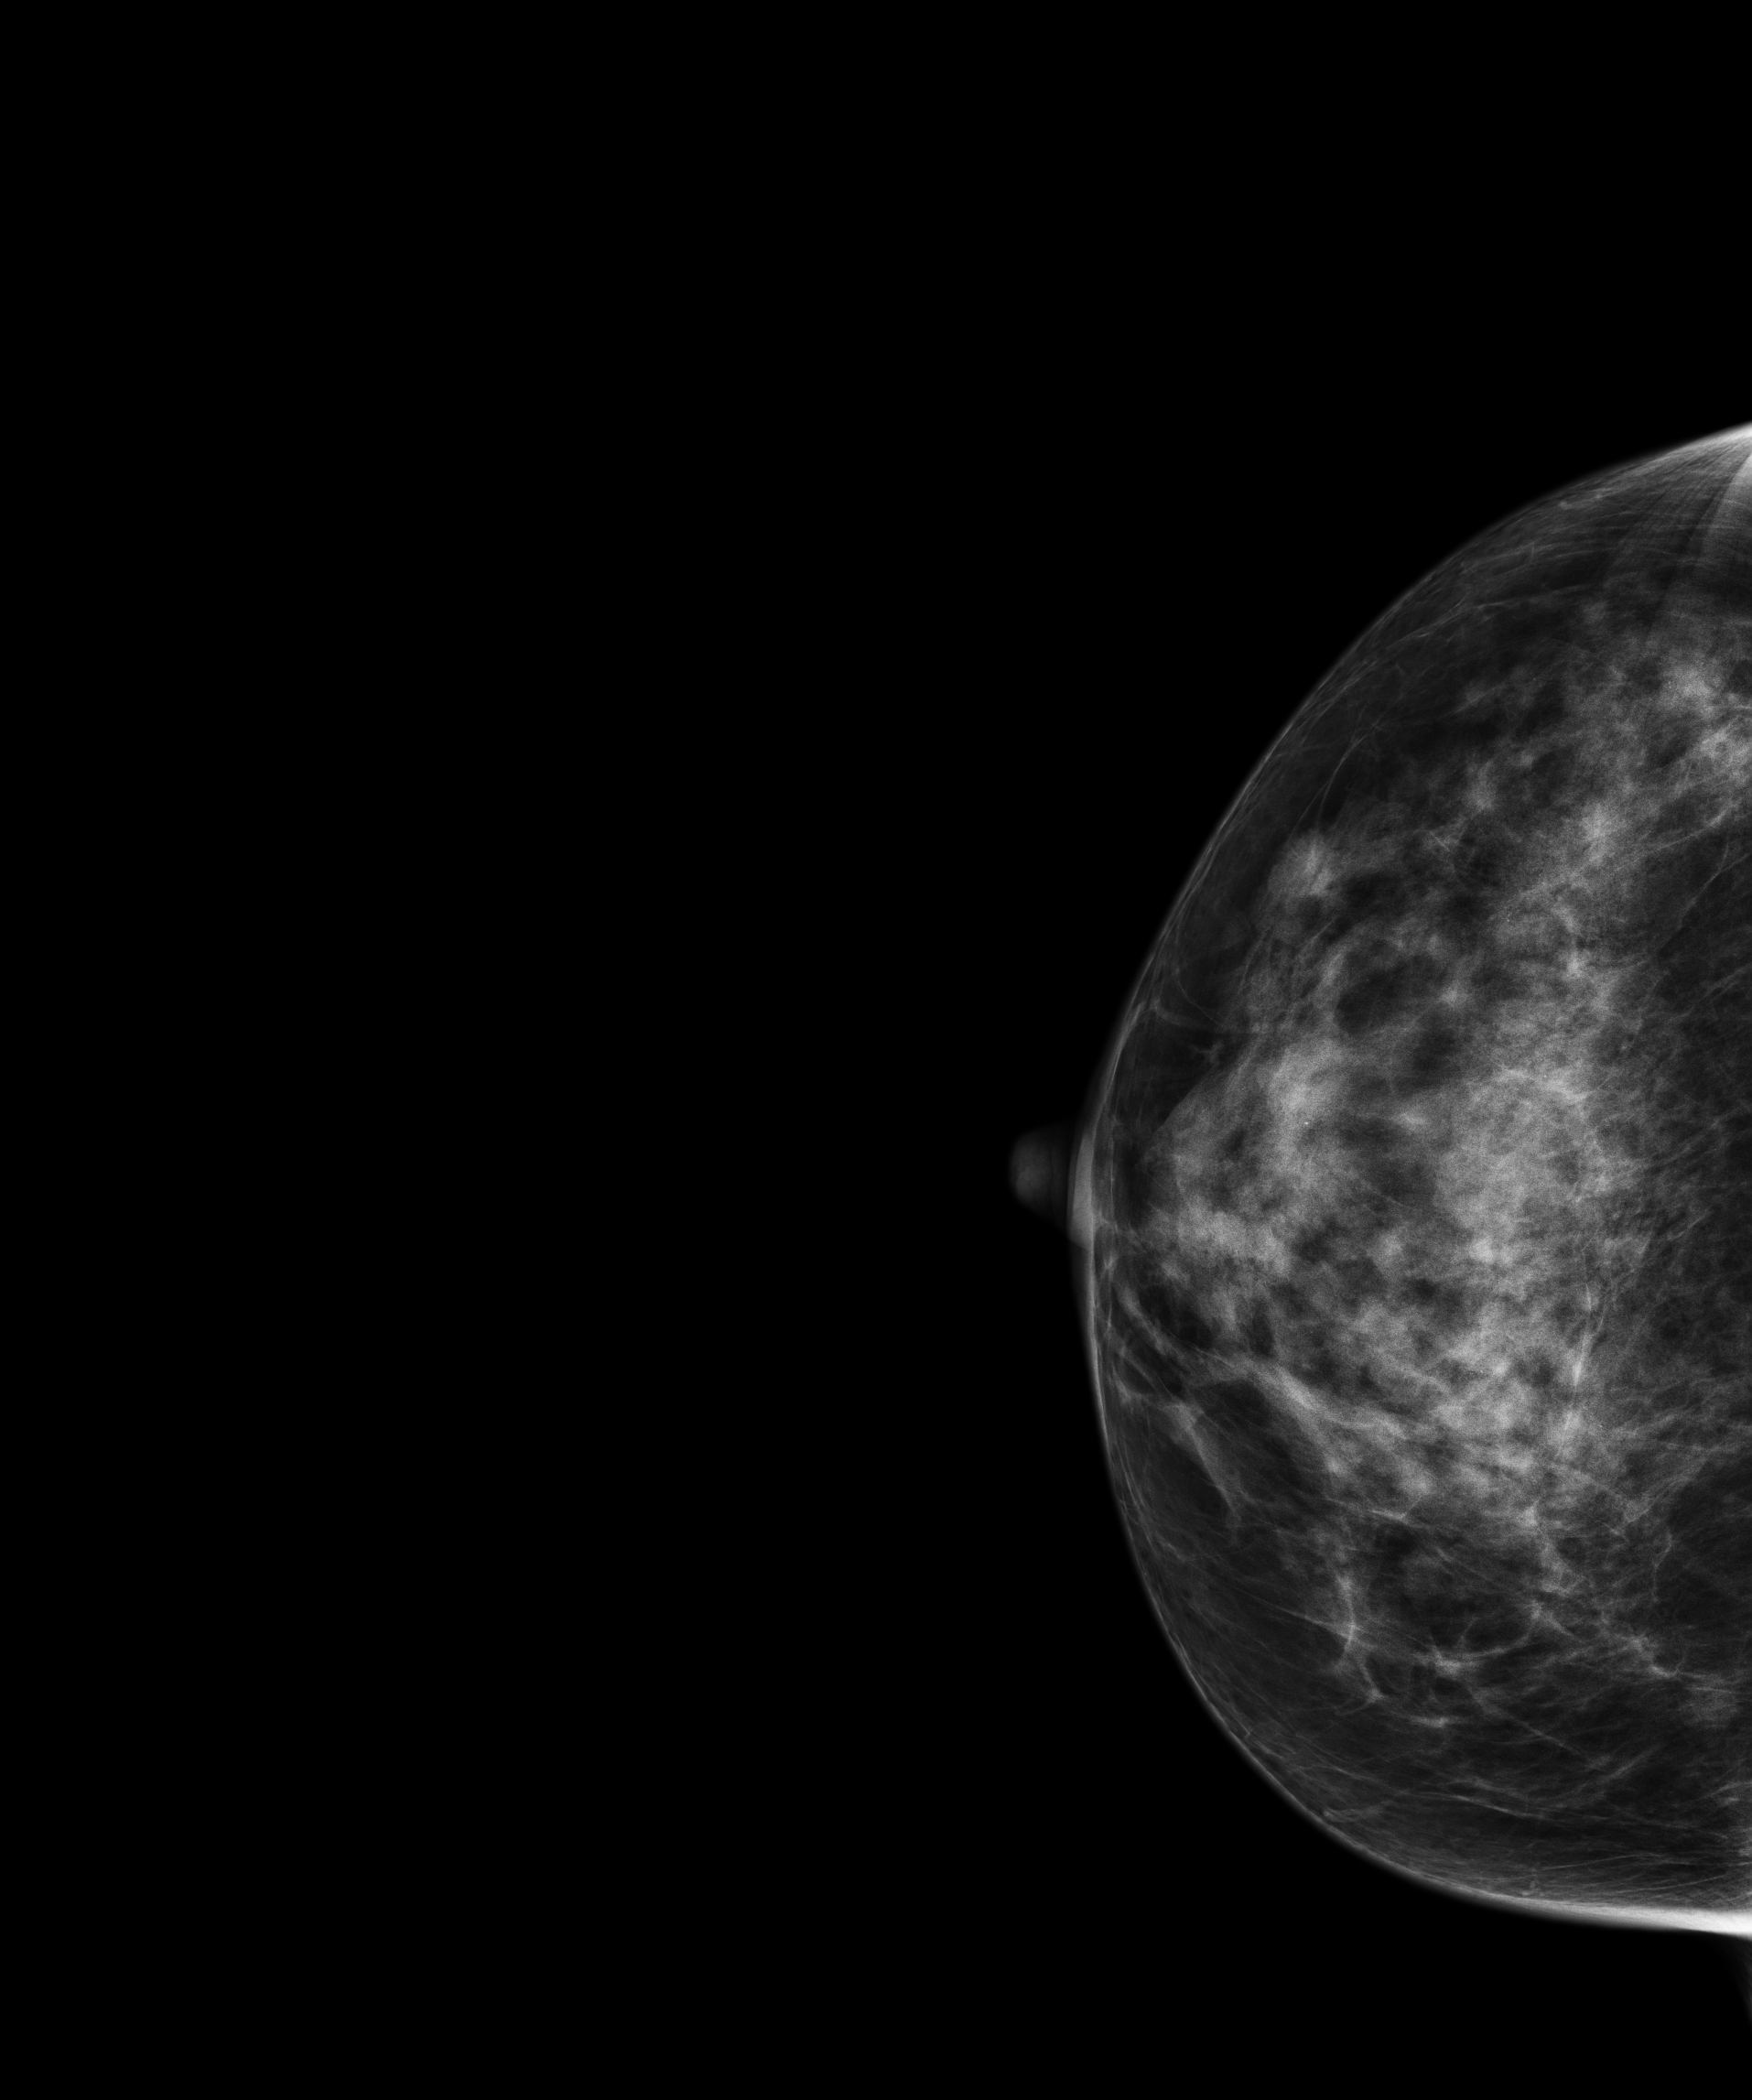
Full-field digital mammogram (FFDM); right breast; cranio-caudal projection; screening examination; system: Senographe Essential ADS_56.21.3. Patient: female, 58 years.
Final BI-RADS category for the screening round (tomosynthesis exam, both breasts): category 1.